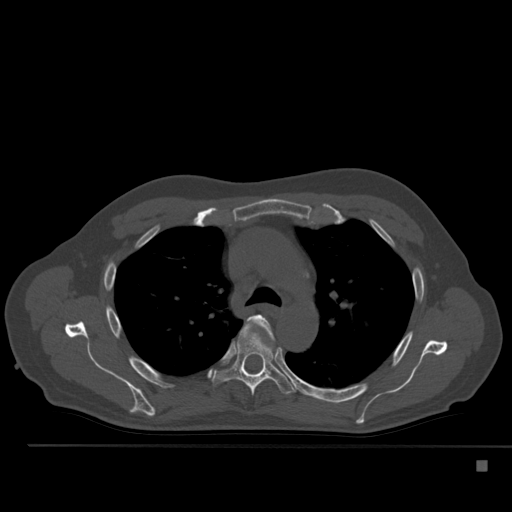
CT including the spine, one axial slice; slice 369 of 517 in the series (ordered by position); 120 kVp; bone window (W 1800 / L 400 HU); 1.5 mm slice thickness; 512 × 512 image matrix. Patient: male, 70 years. From the clinical record (not read from this slice): primary cancer: renal.
Outlined on this slice (semi-automatically segmented with operator editing):
- T4 vertebra: bounding box [x1, y1, x2, y2] px = [248, 314, 273, 337]
- T5 vertebra: [212, 323, 296, 396]